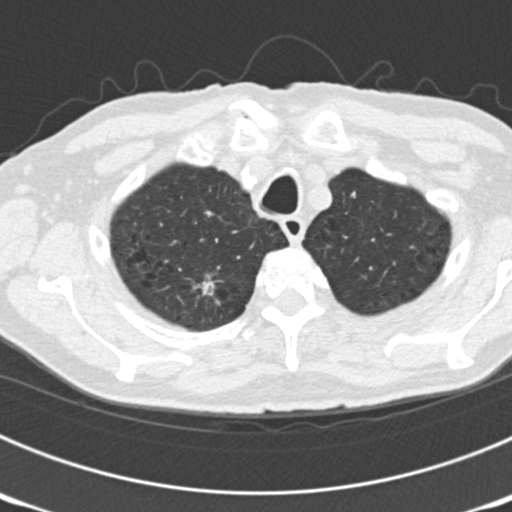
Low-dose screening chest CT, one axial slice; slice 155 of 177 in the series (ordered by position); 120 kVp; lung window (W 1500 / L -600 HU); 2 mm slice thickness; 512 × 512 image matrix, field of view 300 × 300 mm.
Outlined on this slice (manually delineated by an expert):
- lesion 3 (nodule, upper lobe of right lung): bounding box <195,279,216,296> (left, top, right, bottom; pixels)